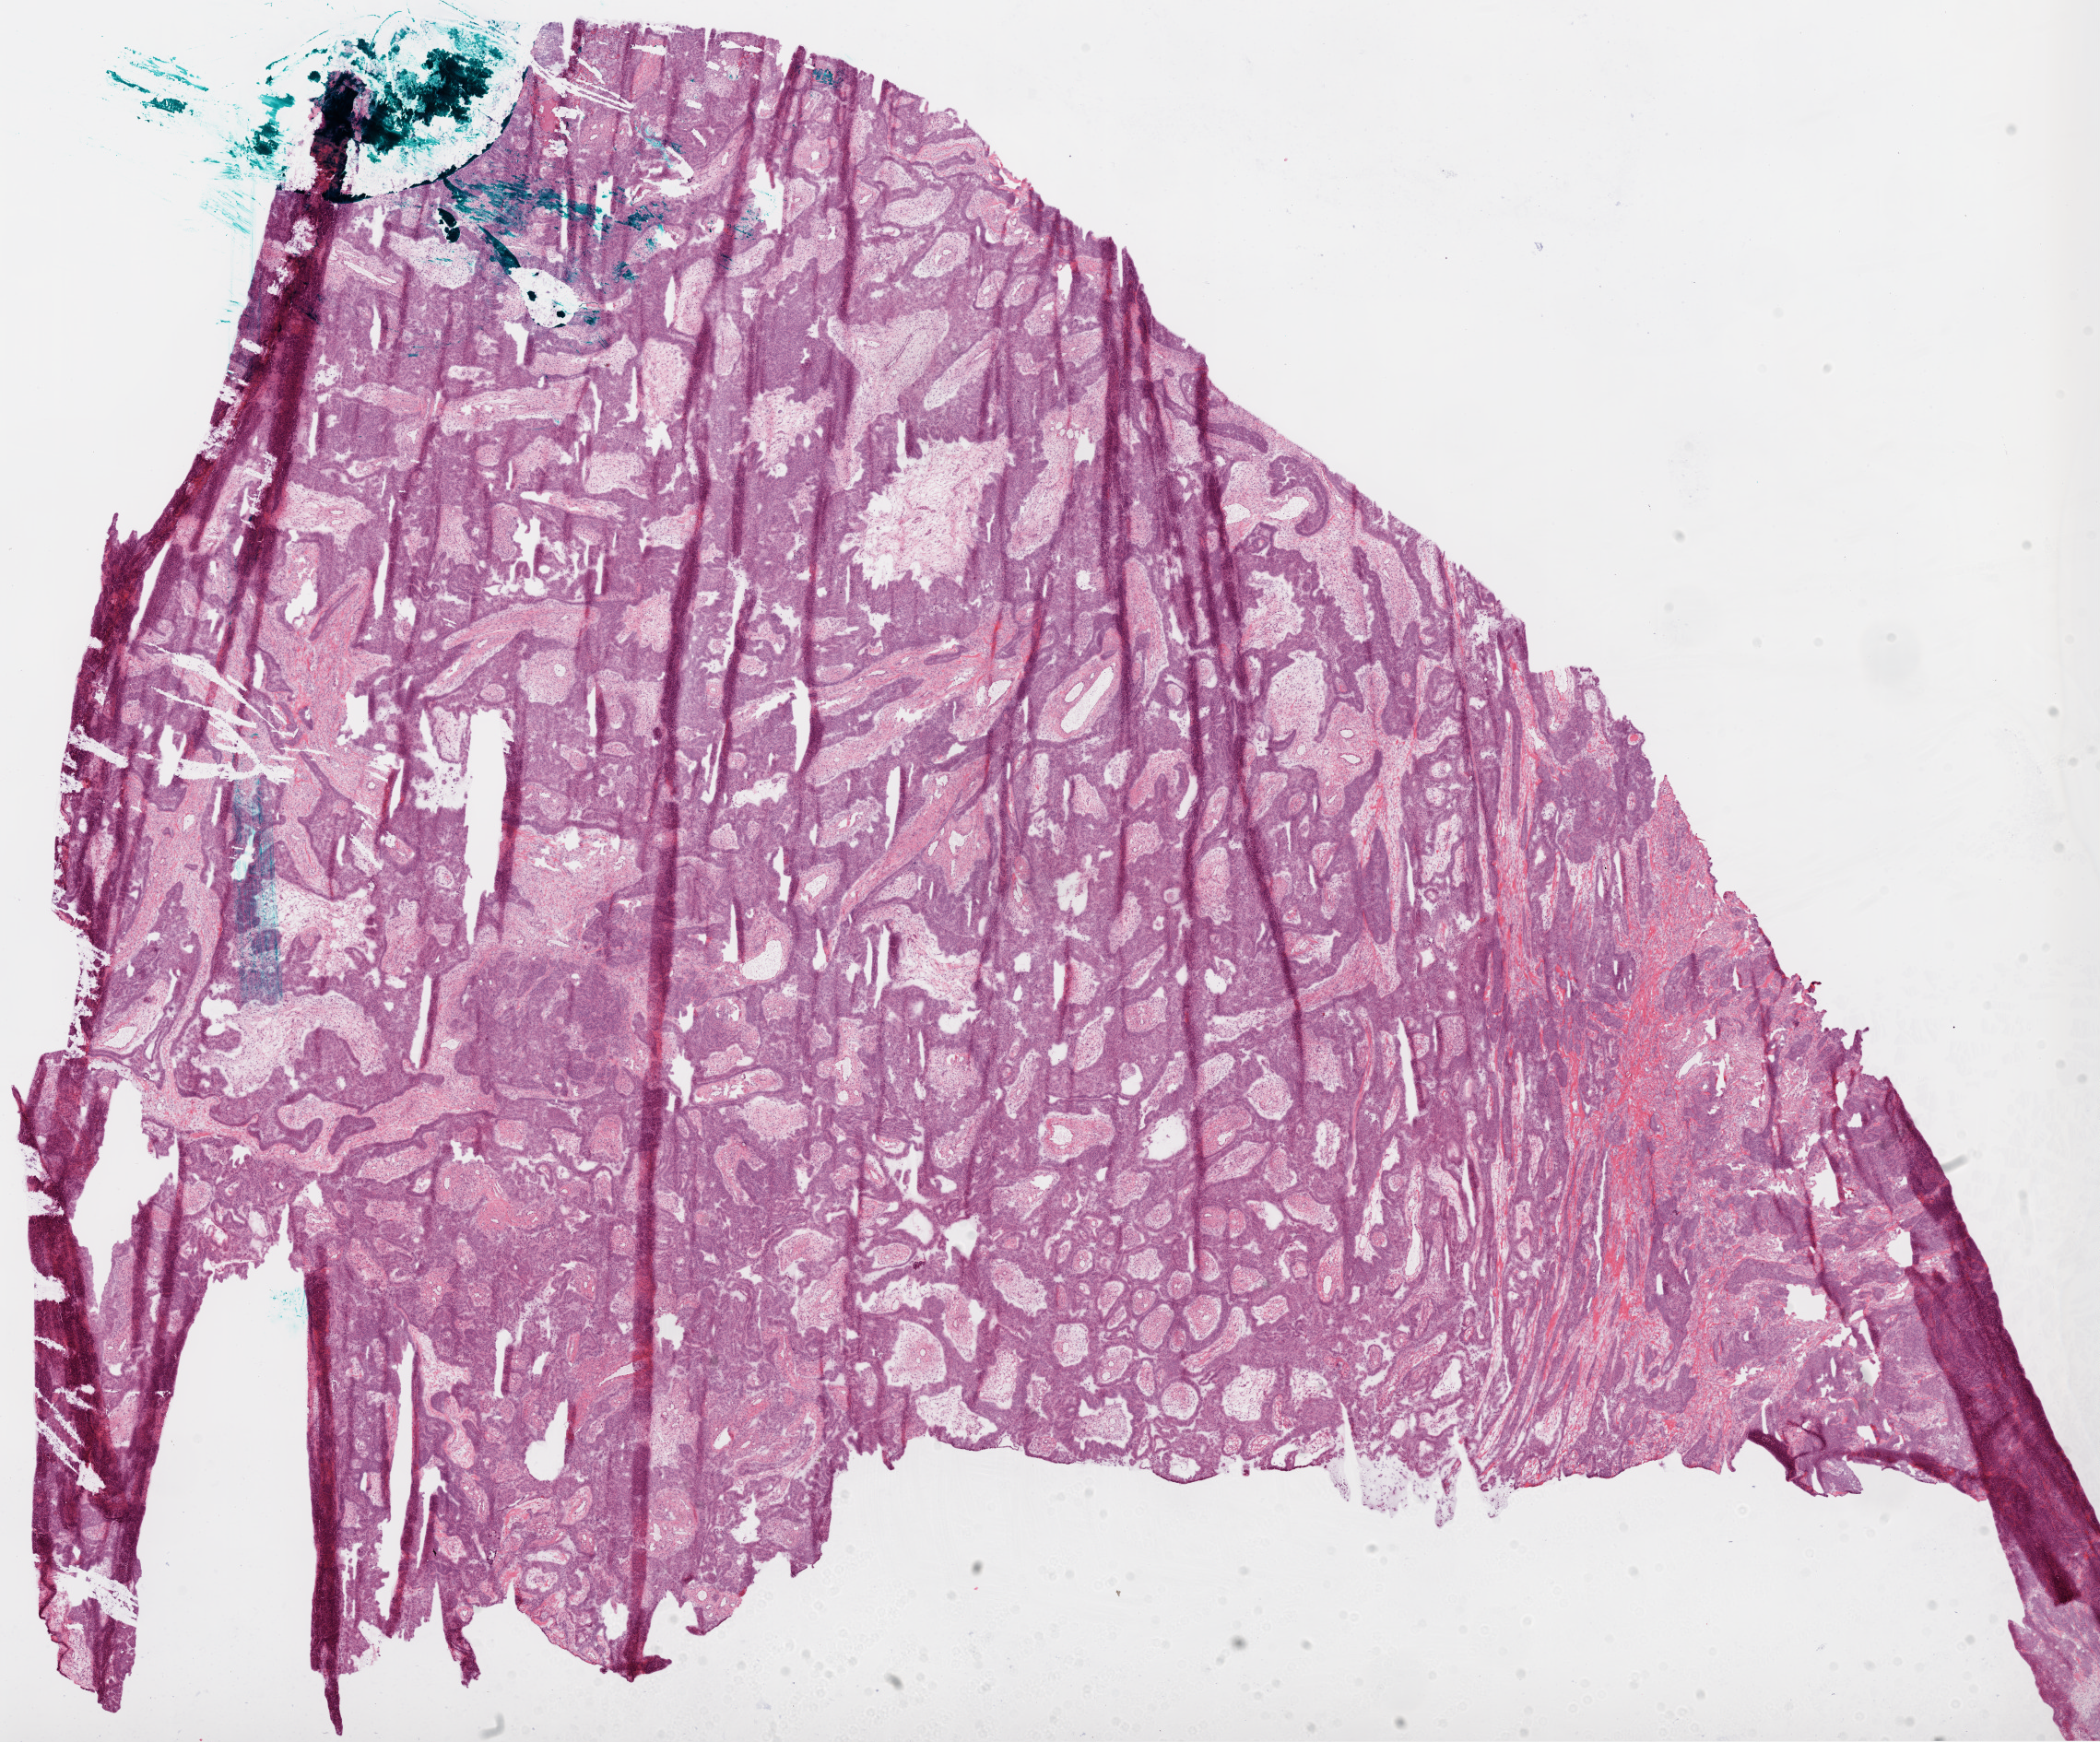
Whole-slide histology image, Hematoxylin and eosin (H&E) stained, whole scanned area (about 18.4 x 15.2 mm) shown as a low-resolution overview; frozen section; primary tumour sample from the ovary. Female patient; age at initial diagnosis 65 years. Histologic grade: G3 (poorly differentiated). Composition of this section per pathologist review: tumour cells 85%, tumour nuclei 90%, normal cells 0%, stromal cells 10%, necrosis 5%.
Histologic diagnosis: Serous cystadenocarcinoma, NOS. FIGO stage: IIIC.